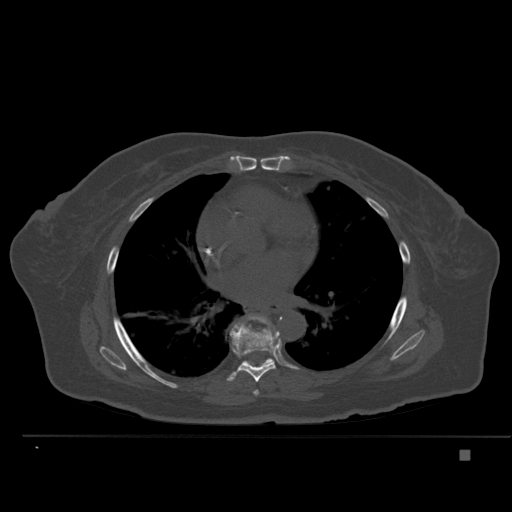
CT including the spine, one axial slice; position 323 of 477 along the scan axis; bone window (W 1800 / L 400 HU); 1.5 mm slice thickness; 512 × 512 image matrix. Patient: female, 74 years. From the clinical record (not read from this slice): primary cancer: colon.
Outlined on this slice (semi-automatic segmentation, software-assisted and operator-edited):
- T6 vertebra: bounding box <253,390,259,396> (left, top, right, bottom; pixels)
- T7 vertebra: <227,320,280,382>
- T8 vertebra: <244,315,274,365>